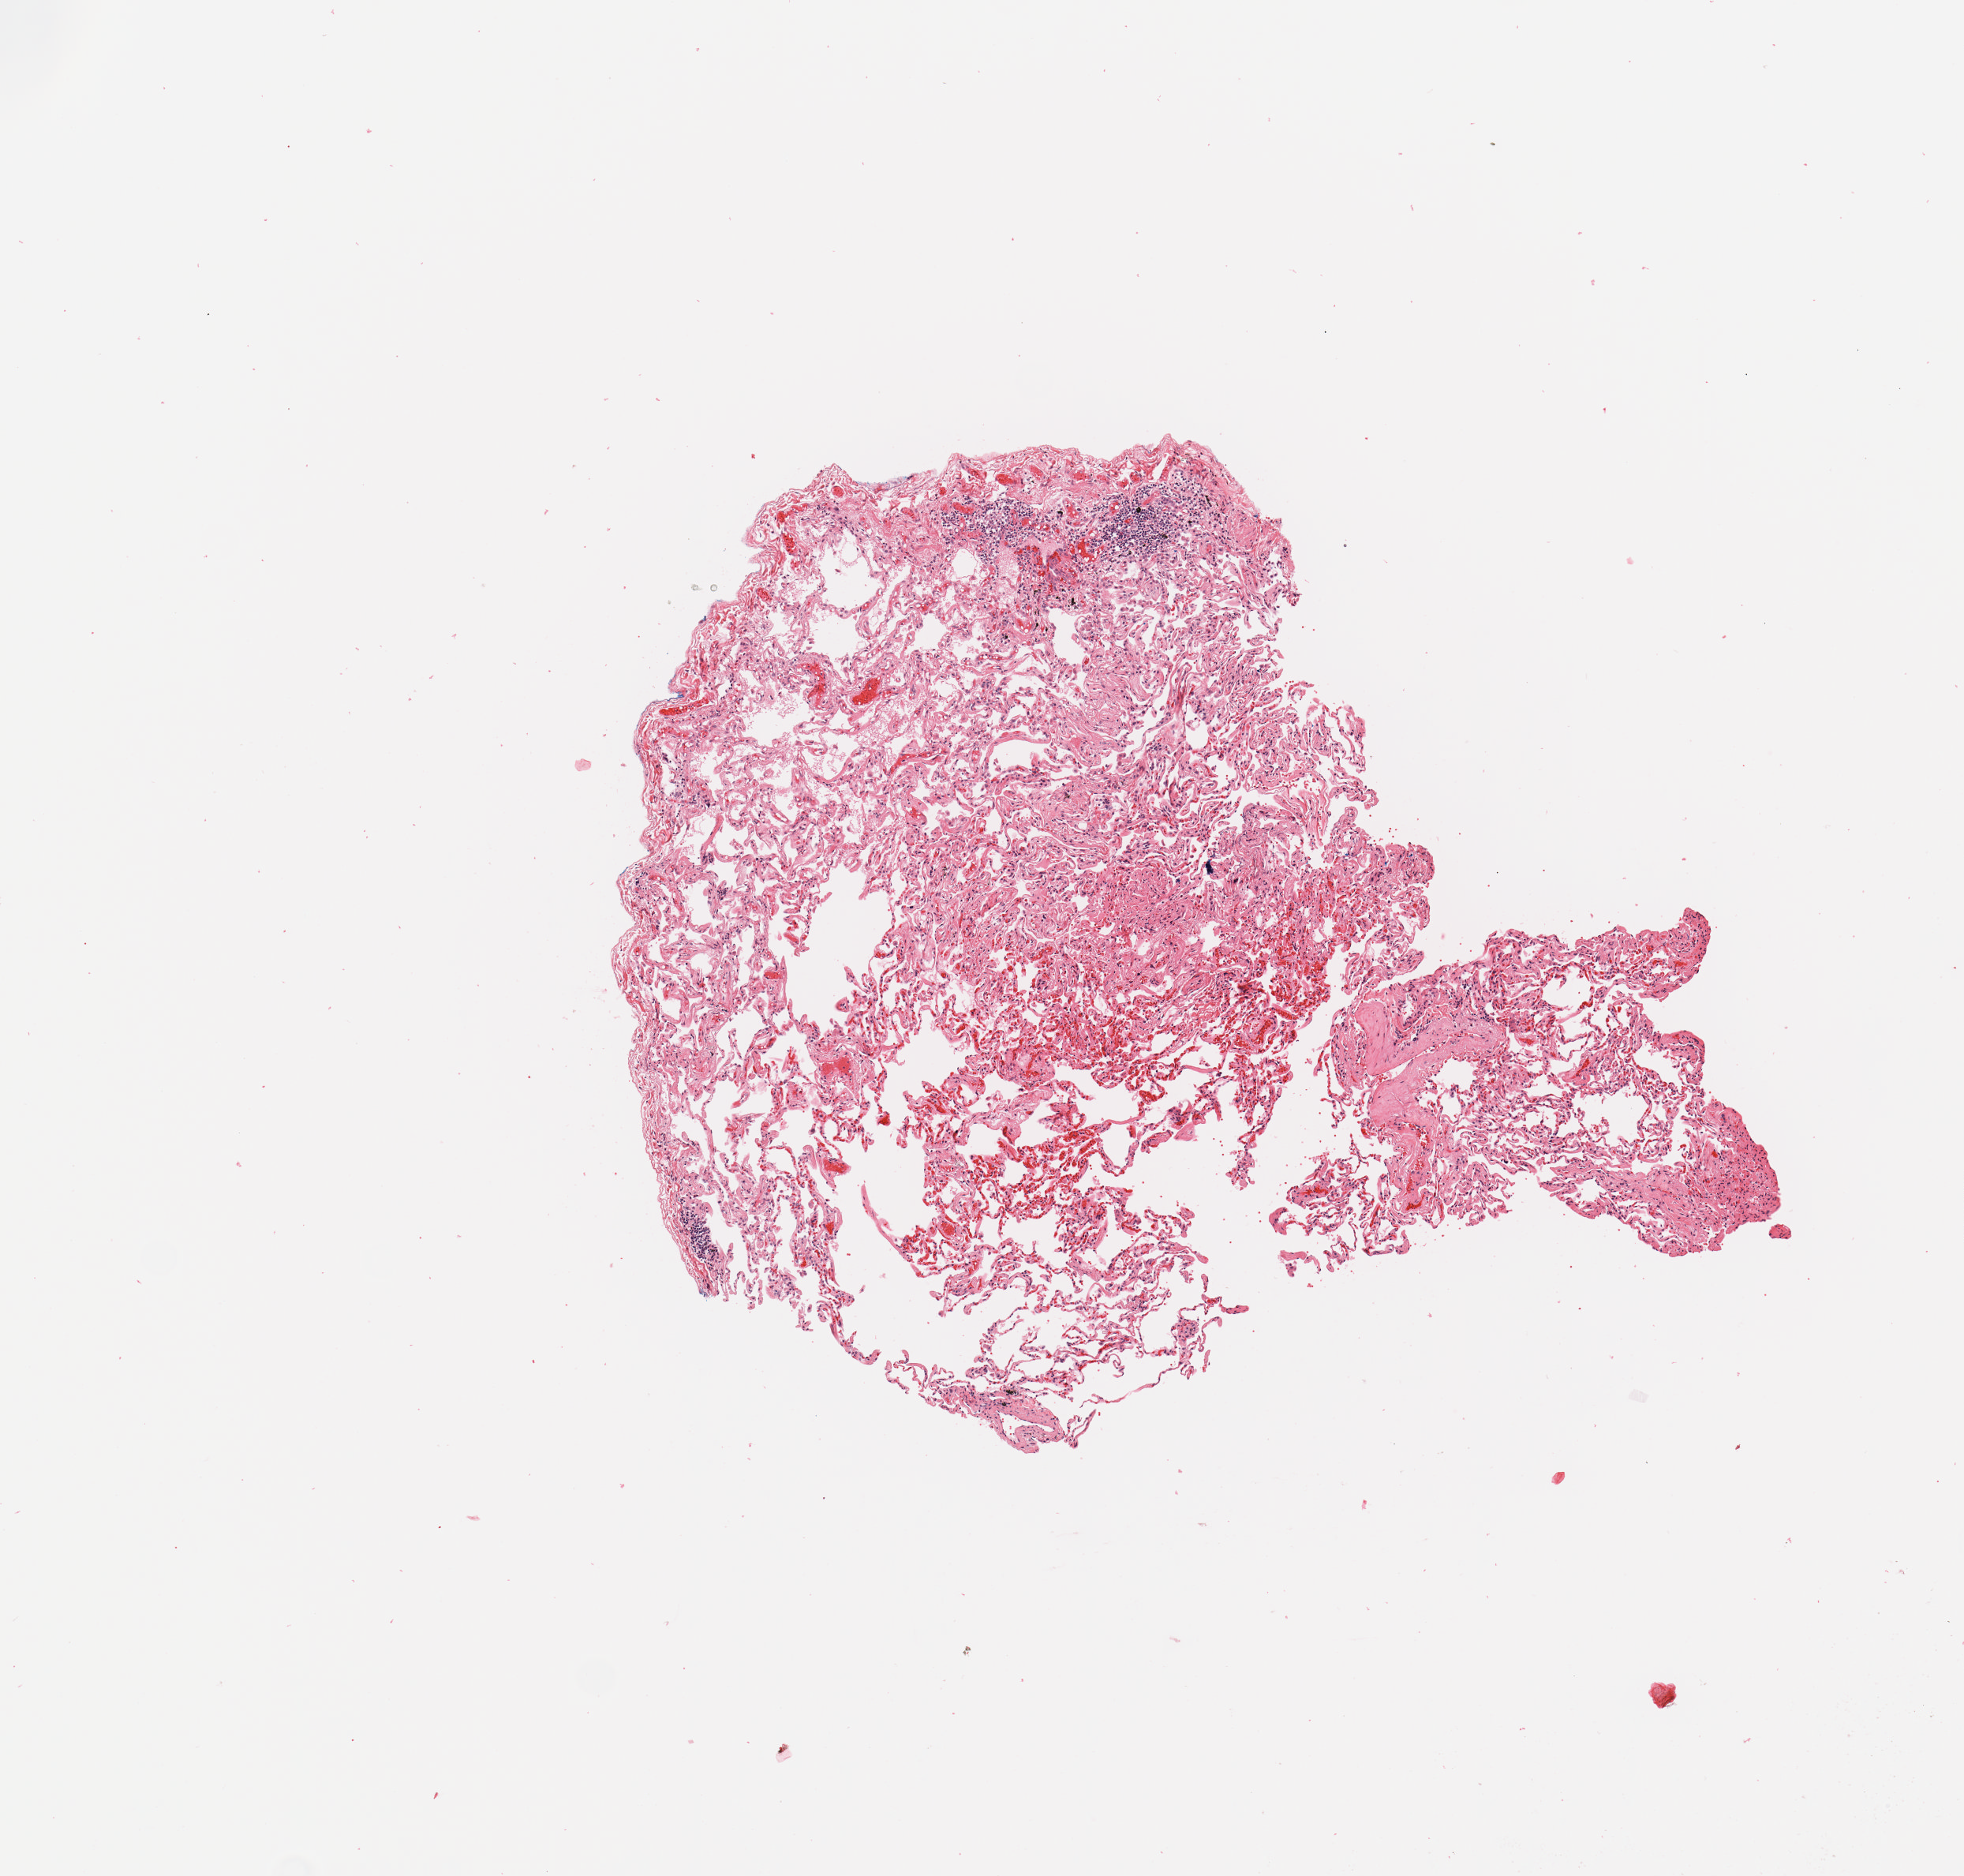
Digitized H&E-stained tissue section (whole slide), whole scanned area (about 4.9 x 4.7 mm) shown as a low-resolution overview; lung, tissue type not recorded.
Patient diagnosis (cohort enrolment): lung adenocarcinoma (lung).